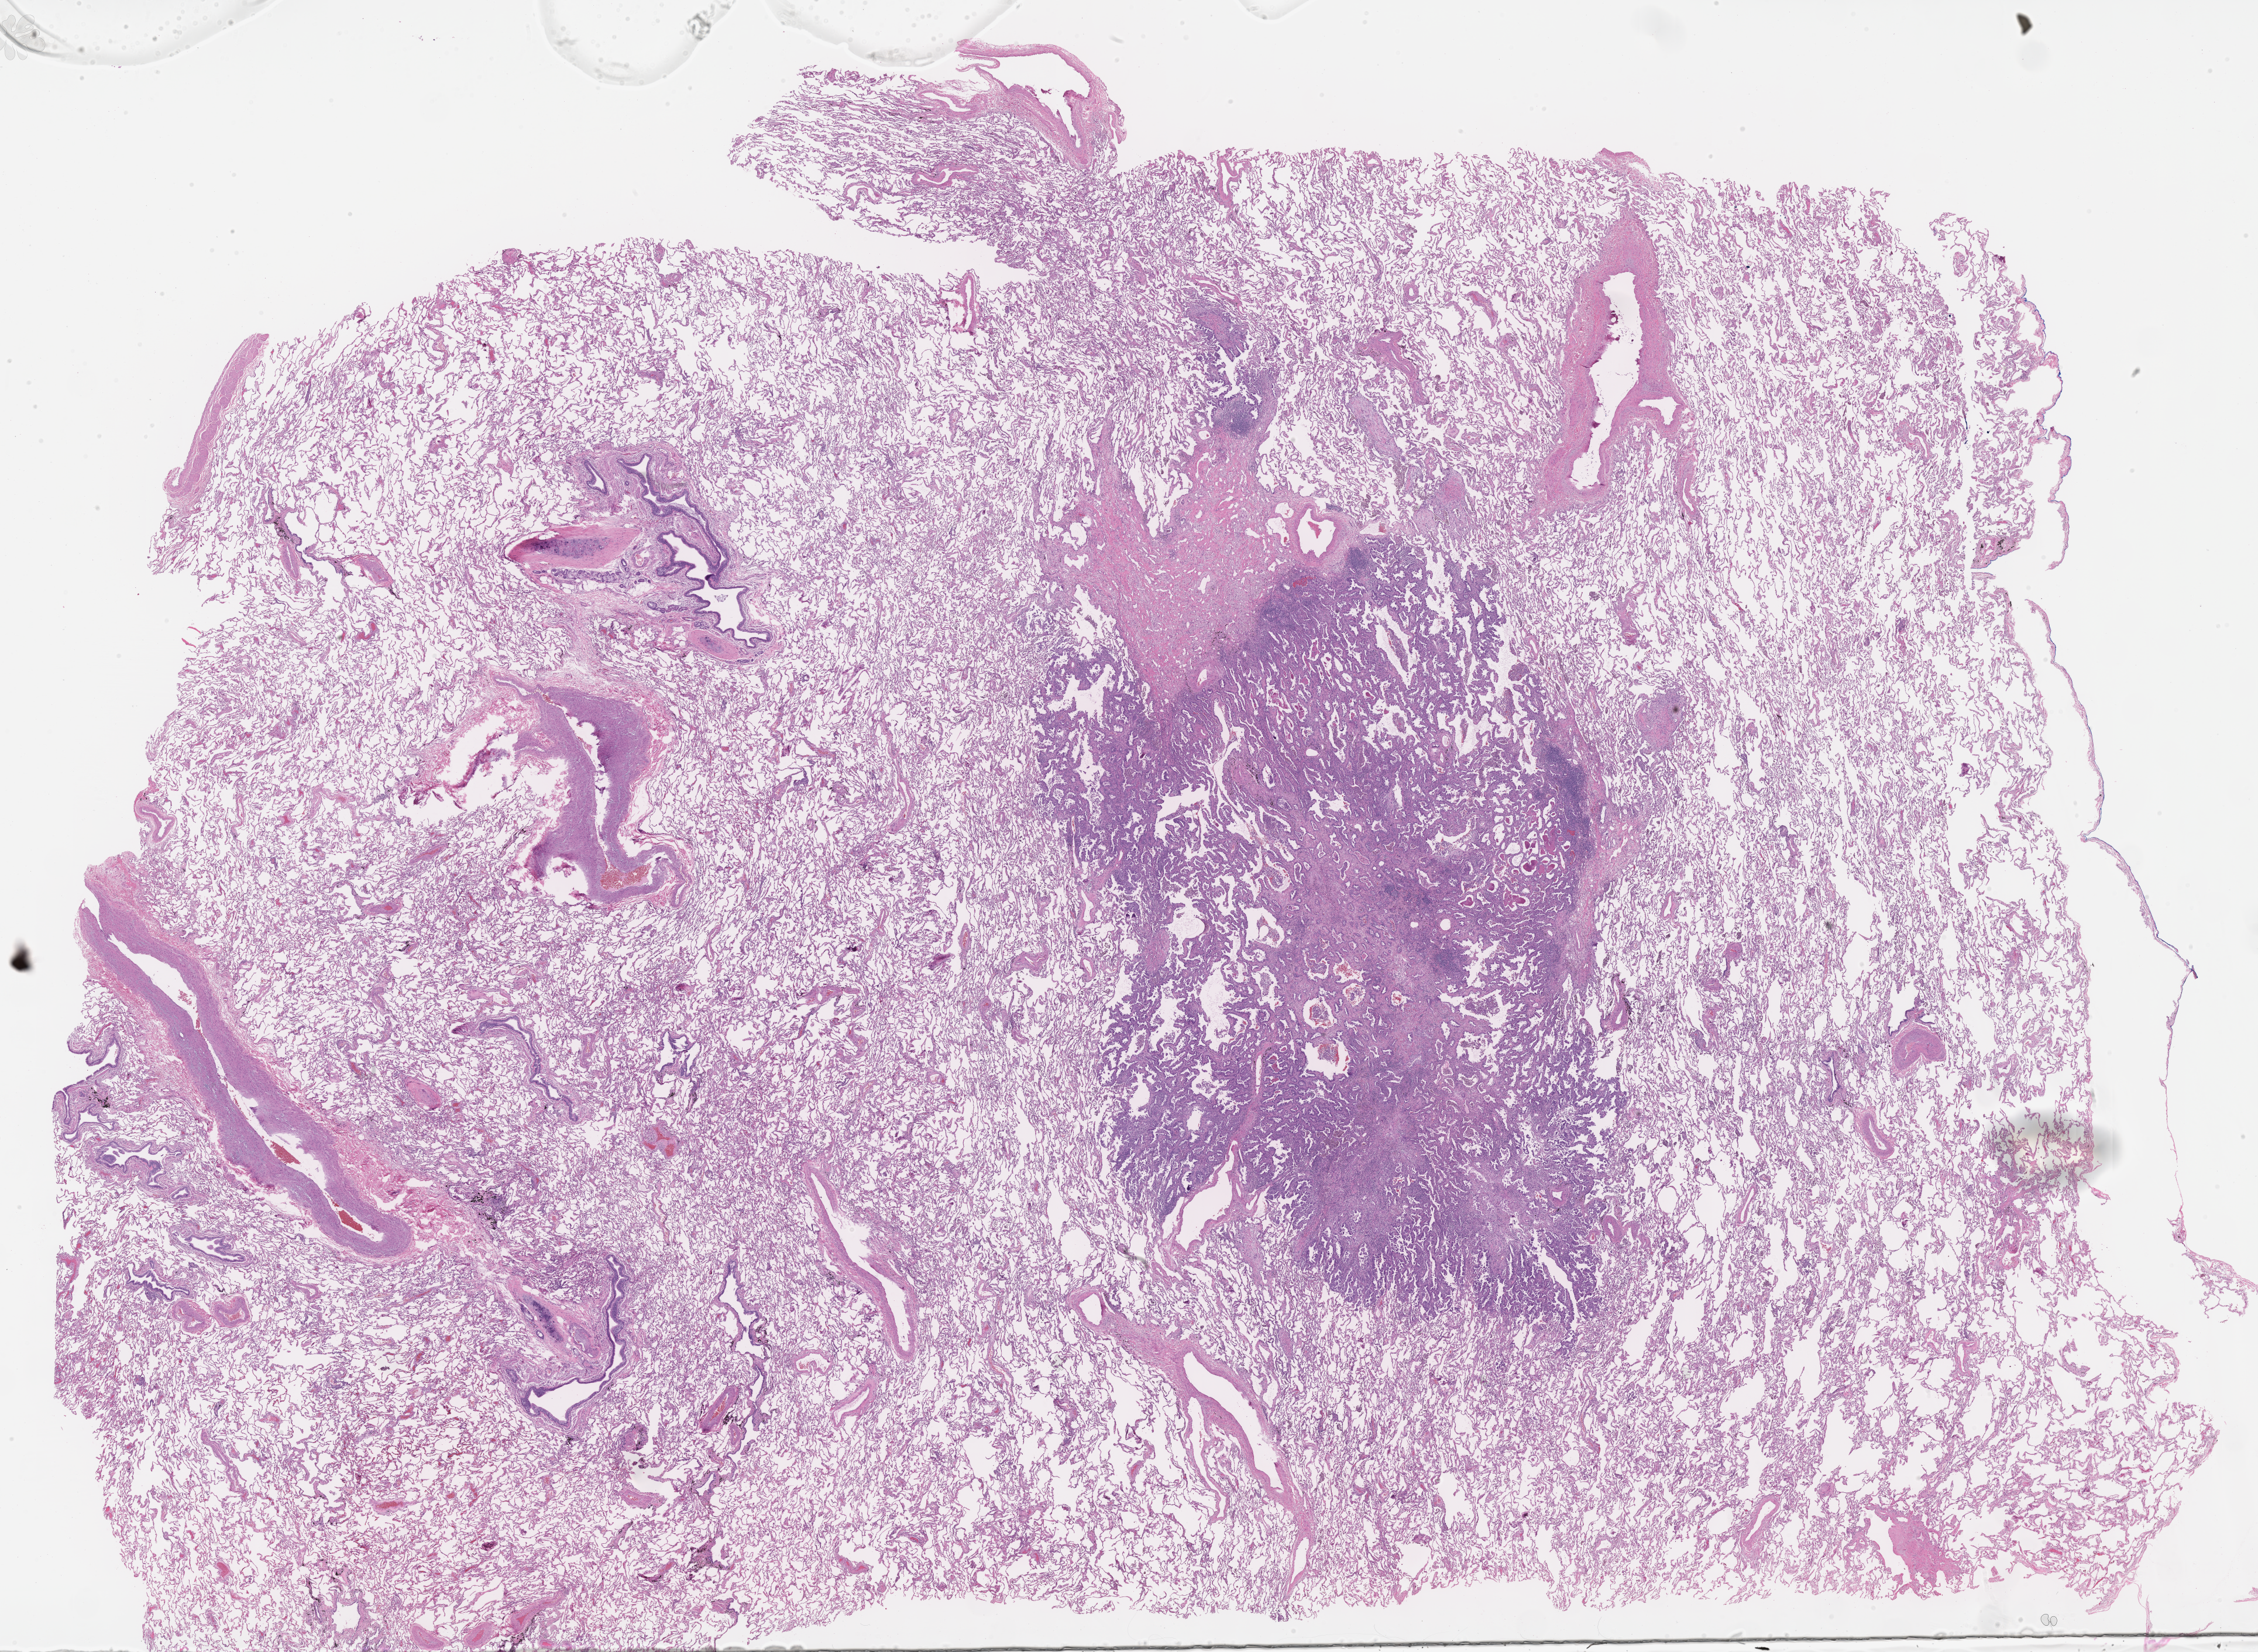
H&E whole-slide image — a low-resolution overview of the entire scanned area, about 31.1 x 22.8 mm, formalin-fixed paraffin-embedded section, specimen: primary tumor, site: upper lobe of left lung. Male, age 83 years at initial diagnosis. Composition of this section per pathologist review: tumor cells 20%, tumor nuclei 30%.
Diagnosis: Acinar cell carcinoma.